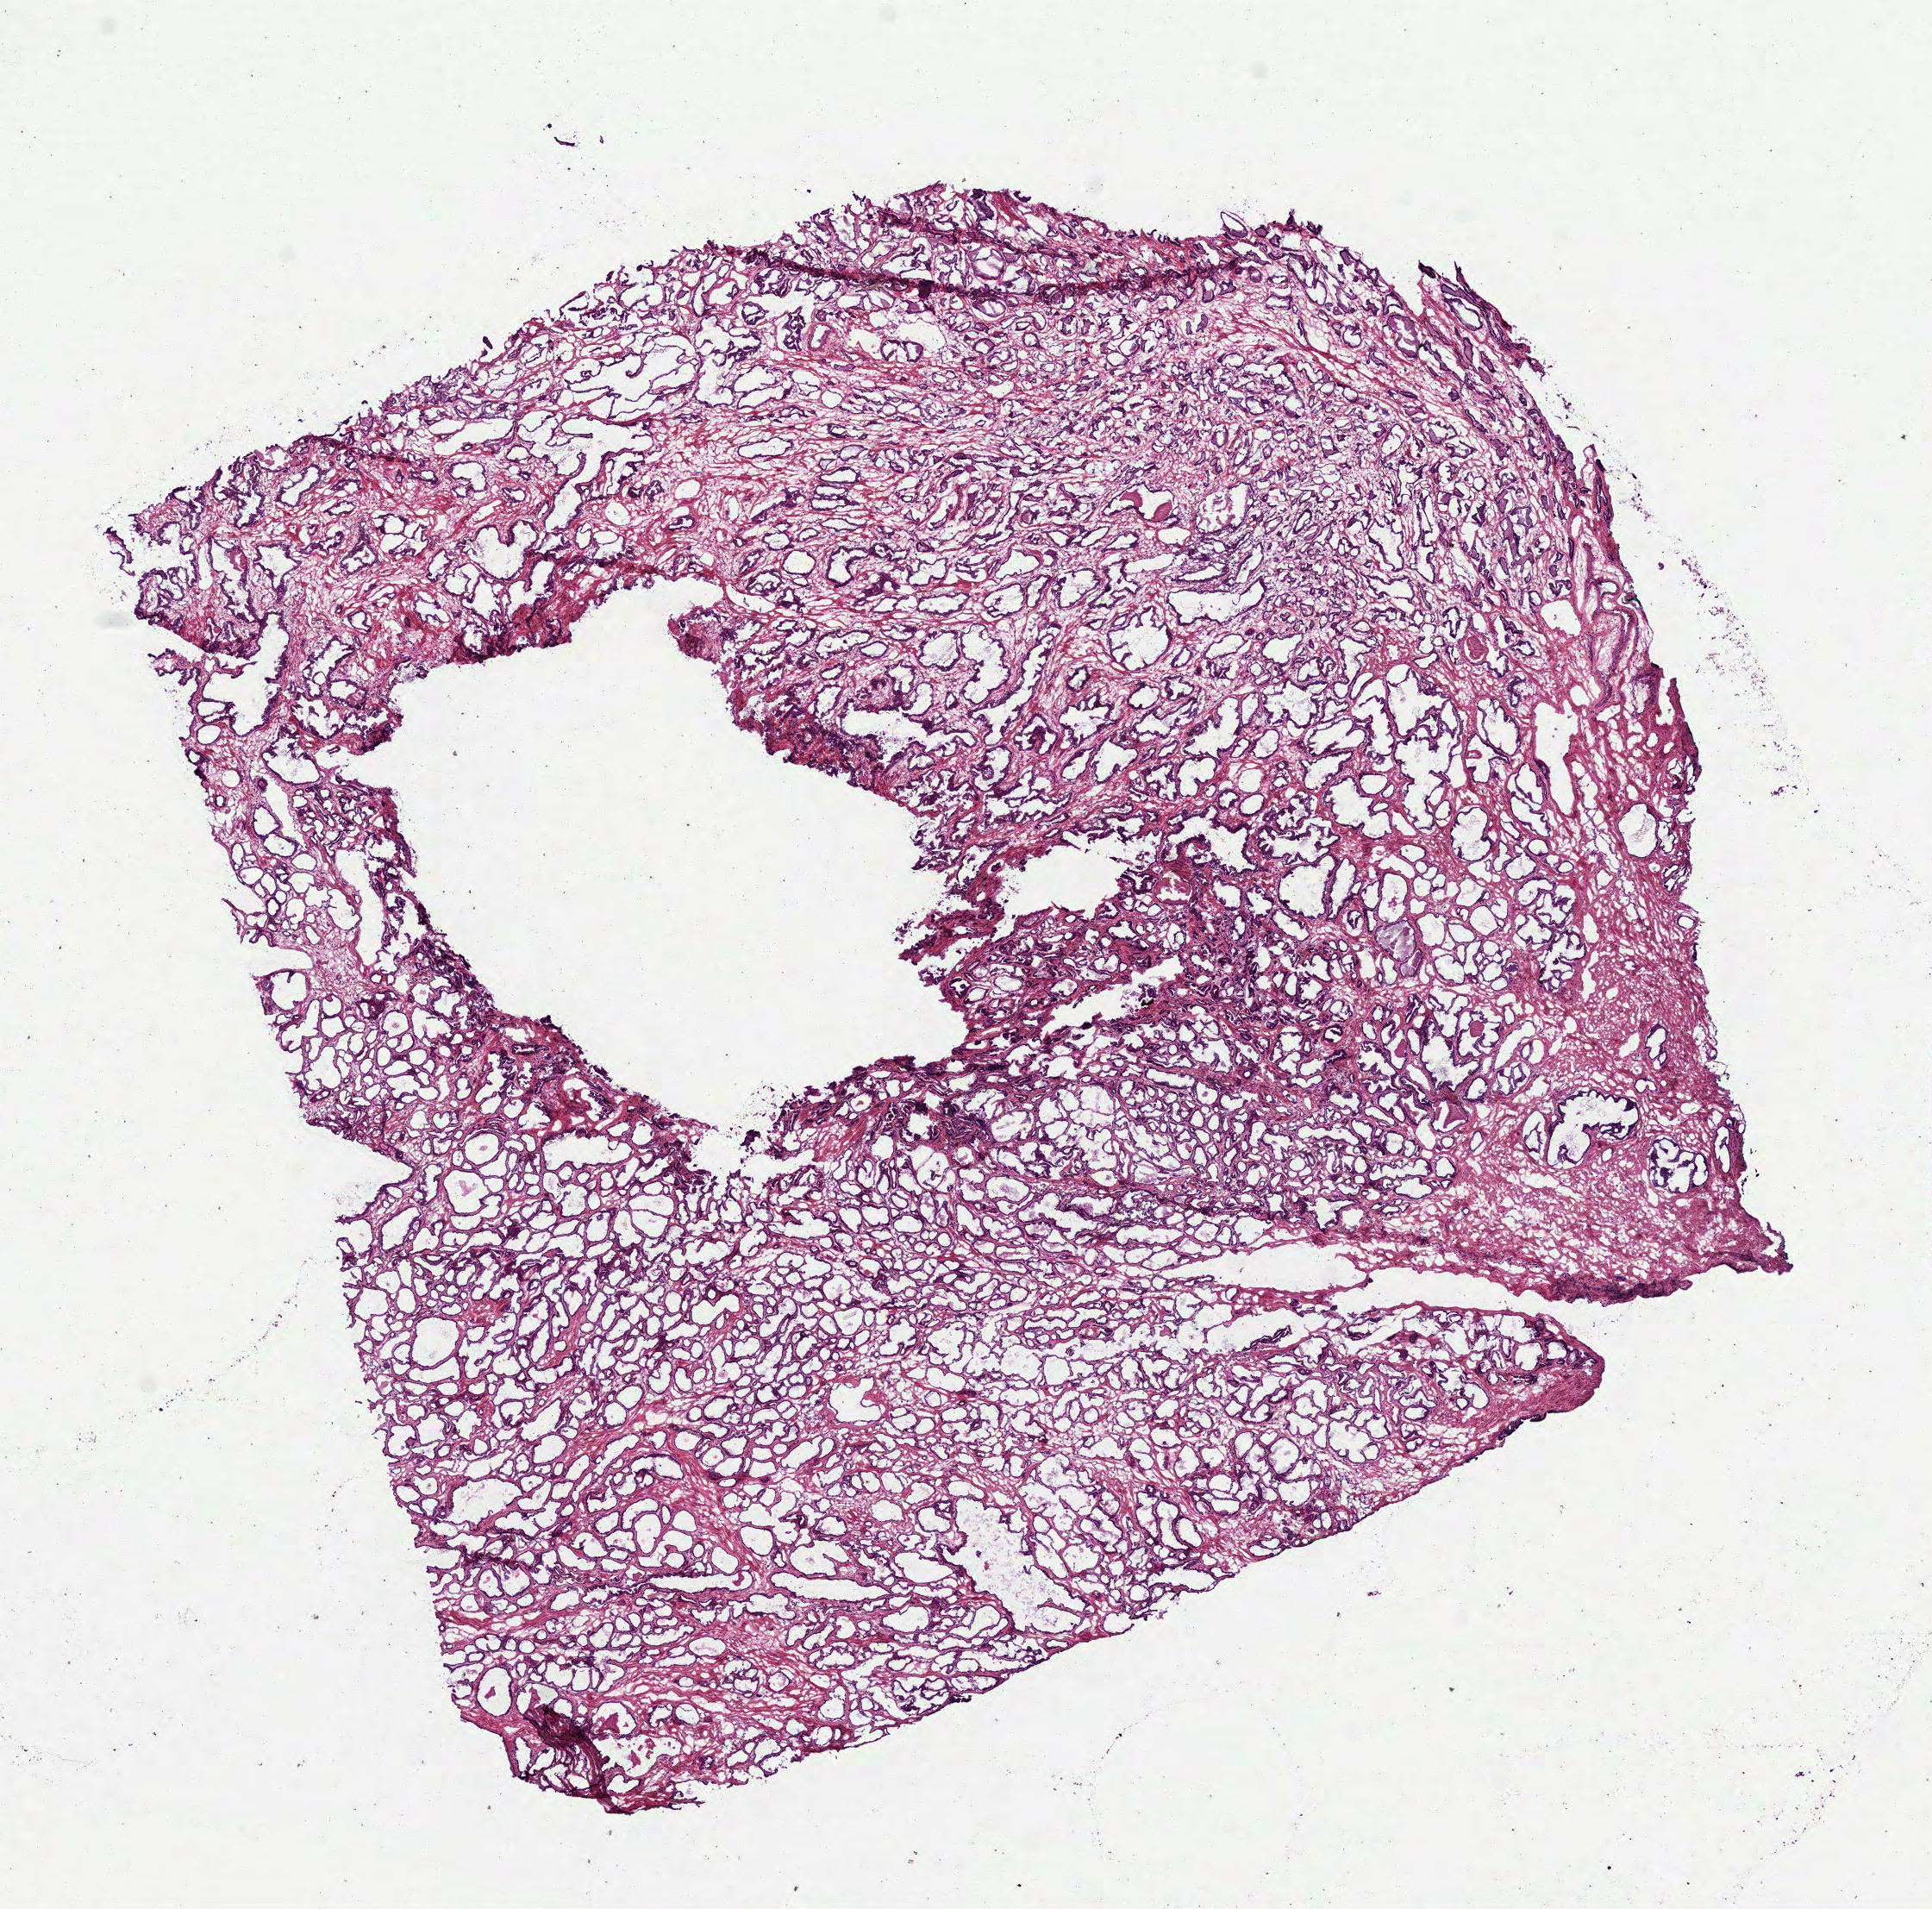
H&E whole-slide image — shown as a low-resolution overview of the whole scanned area (about 9.0 x 8.9 mm, acquisition: 40x scan), frozen section from the bottom of the tissue portion, prostate, primary tumour sample. Male, age 58 years at initial diagnosis. Gleason score: 7 (3+4). Composition of this section per pathologist review: tumour cells 60%, tumour nuclei 65%, normal cells 15%, stromal cells 25%, necrosis 0%. Inflammatory infiltration, as recorded: lymphocyte infiltration 0%, monocyte infiltration 0%, neutrophil infiltration 0%.
Pathologic diagnosis: Acinar cell carcinoma. Laterality: bilateral.